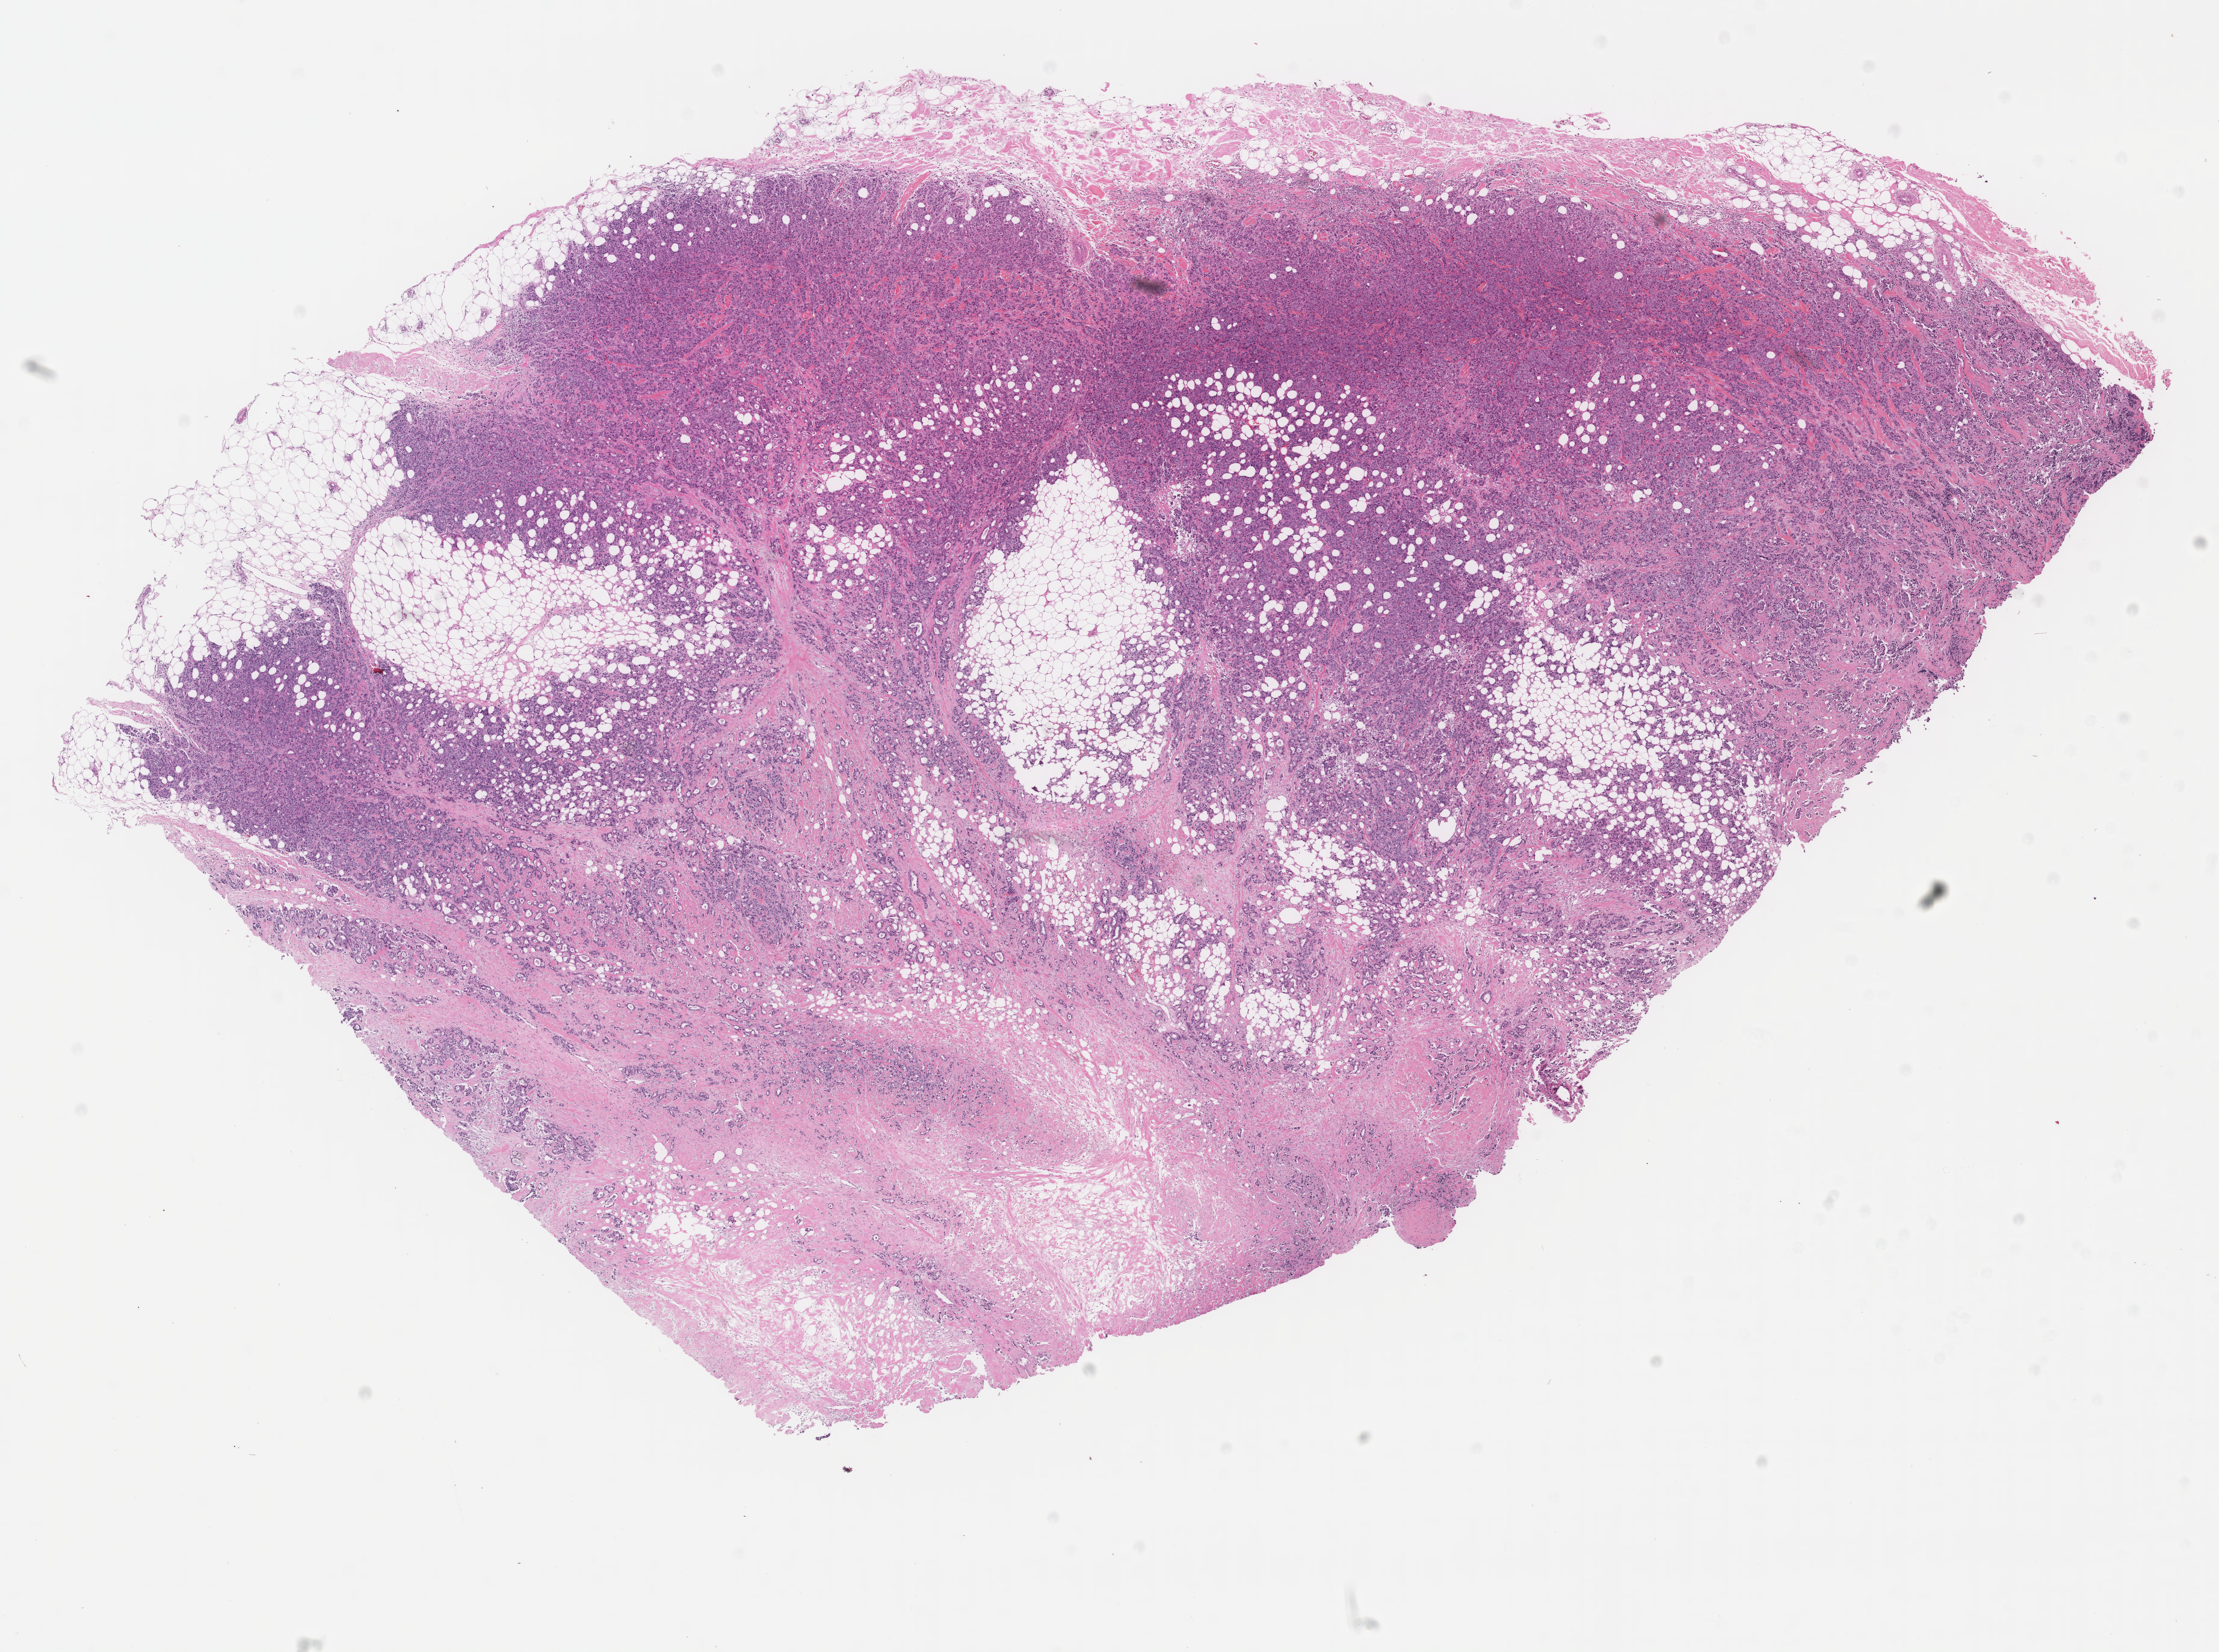
Hematoxylin and eosin (H&E) stained whole-slide image, low-resolution overview of the scanned area, about 14.6 x 10.9 mm (acquisition: 40x scan), formalin-fixed paraffin-embedded (FFPE) diagnostic section, sample: primary tumour, breast. Female patient; age at initial diagnosis 70 years.
* AJCC pathologic stage: IIIA
* TNM: T2 N2 M0
* lymph nodes positive (case pathology): 4 of 9 examined
* diagnosis: Infiltrating duct carcinoma, NOS
* laterality: left